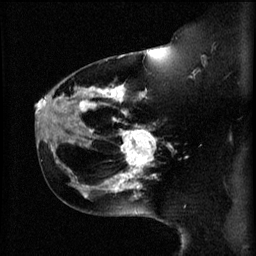
Breast MRI (dynamic contrast-enhanced), one sagittal slice. Position 41 of 60 along the scan axis. 3 images stored at this slice position (order not interpretable as contrast timing). 1.5 T. TE 4.2 ms, TR 11 ms. 2 mm slice thickness. 256 × 256 image matrix, field of view 180 × 180 mm. Patient: female, 44 years.
Annotated regions visible in this slice (semi-automatically segmented with operator editing):
- analysis volume of interest (the breast-tissue region the enhancement analysis was run in; not a lesion): bounding box (x1, y1, x2, y2) in pixels: (112, 124, 159, 179)
- tumour enhancement mask (voxels above the 70 % enhancement threshold inside the analysis volume of interest): (112, 130, 157, 179)